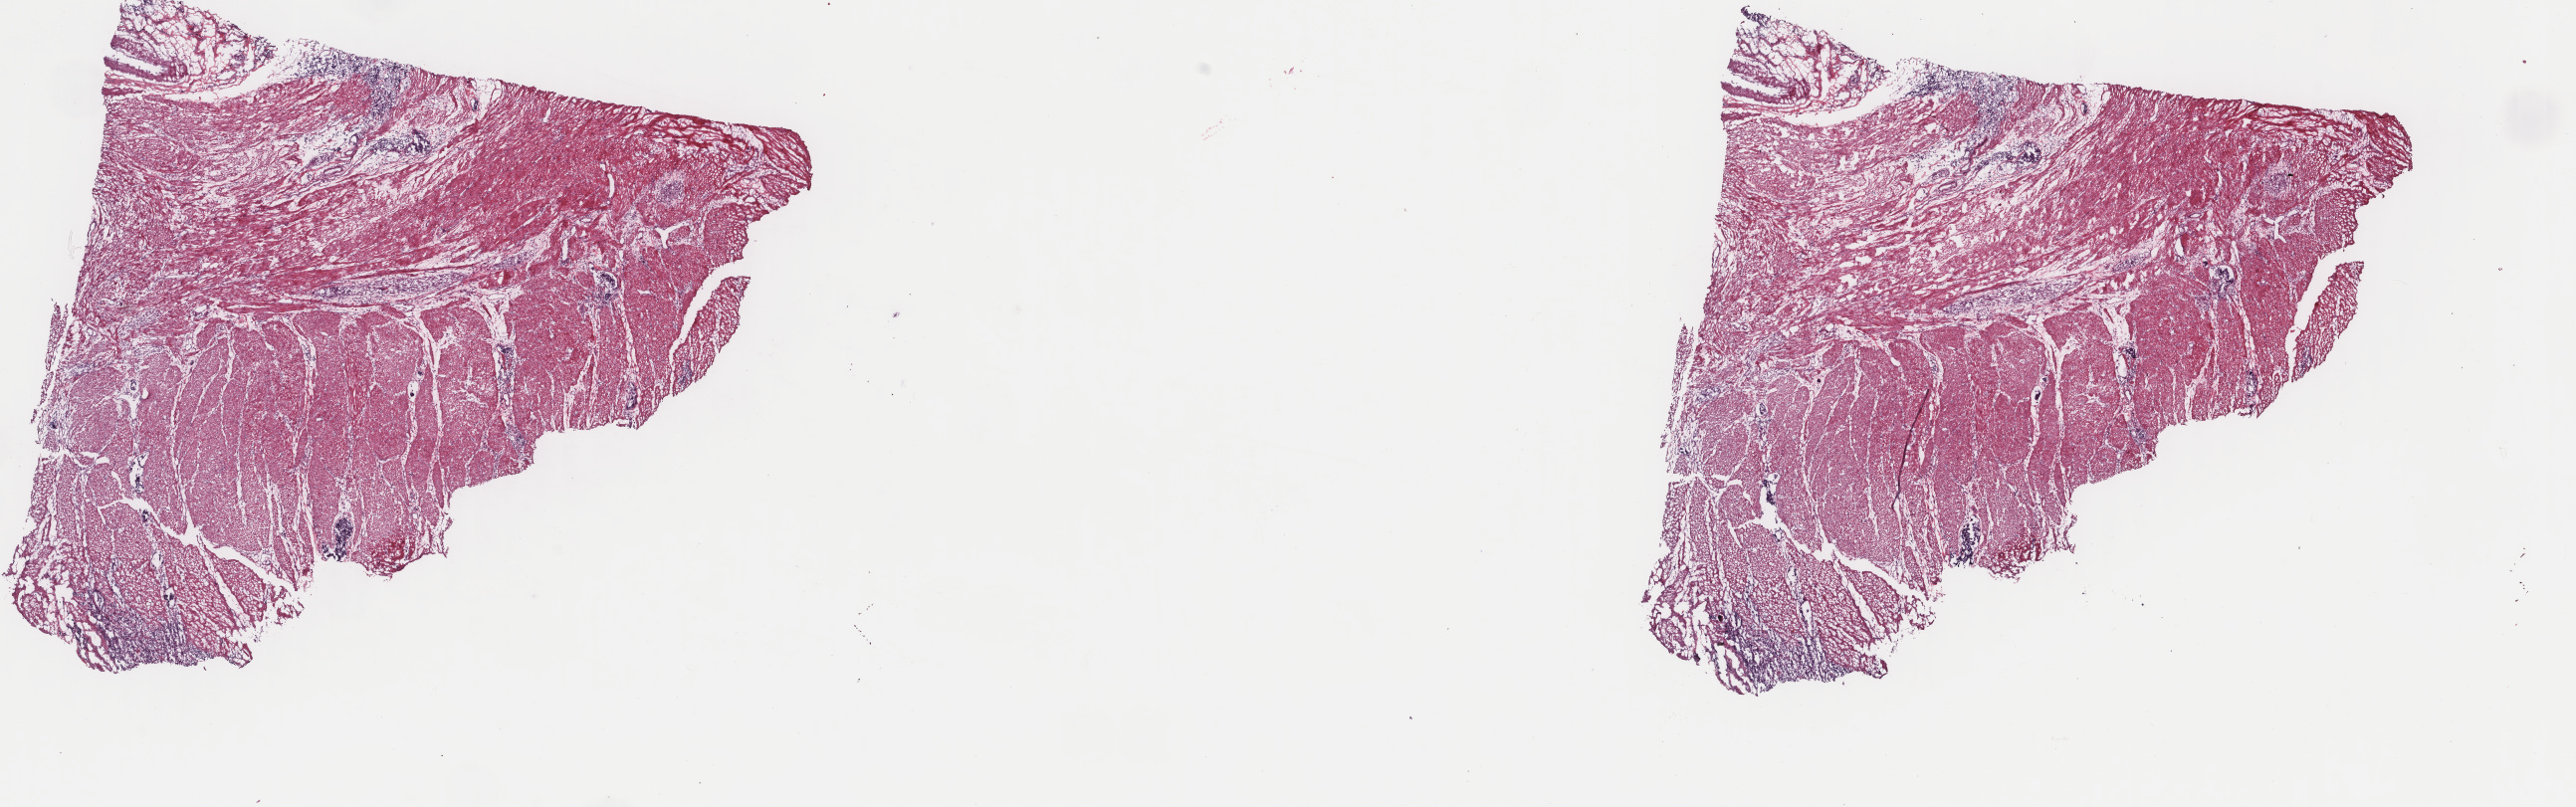
Whole-slide histology image, H&E — shown as a low-resolution overview of the whole scanned area (about 20.5 x 6.4 mm, acquisition: 40x scan). Frozen section from the top of the tissue portion. Stomach, primary tumour sample. Male, age 51 years at initial diagnosis. Histologic grade: G3 (poorly differentiated). Slide review estimates, as recorded: tumour cells 60%, tumour nuclei 60%, normal cells 0%, stromal cells 40%, necrosis 0%. Infiltration values recorded for this section: lymphocyte infiltration 5%, monocyte infiltration 2%, neutrophil infiltration 1%.
• AJCC pathologic stage: IV (7th edition)
• histologic diagnosis: Signet ring cell carcinoma (gastric antrum)
• TNM: T4a N3a M1